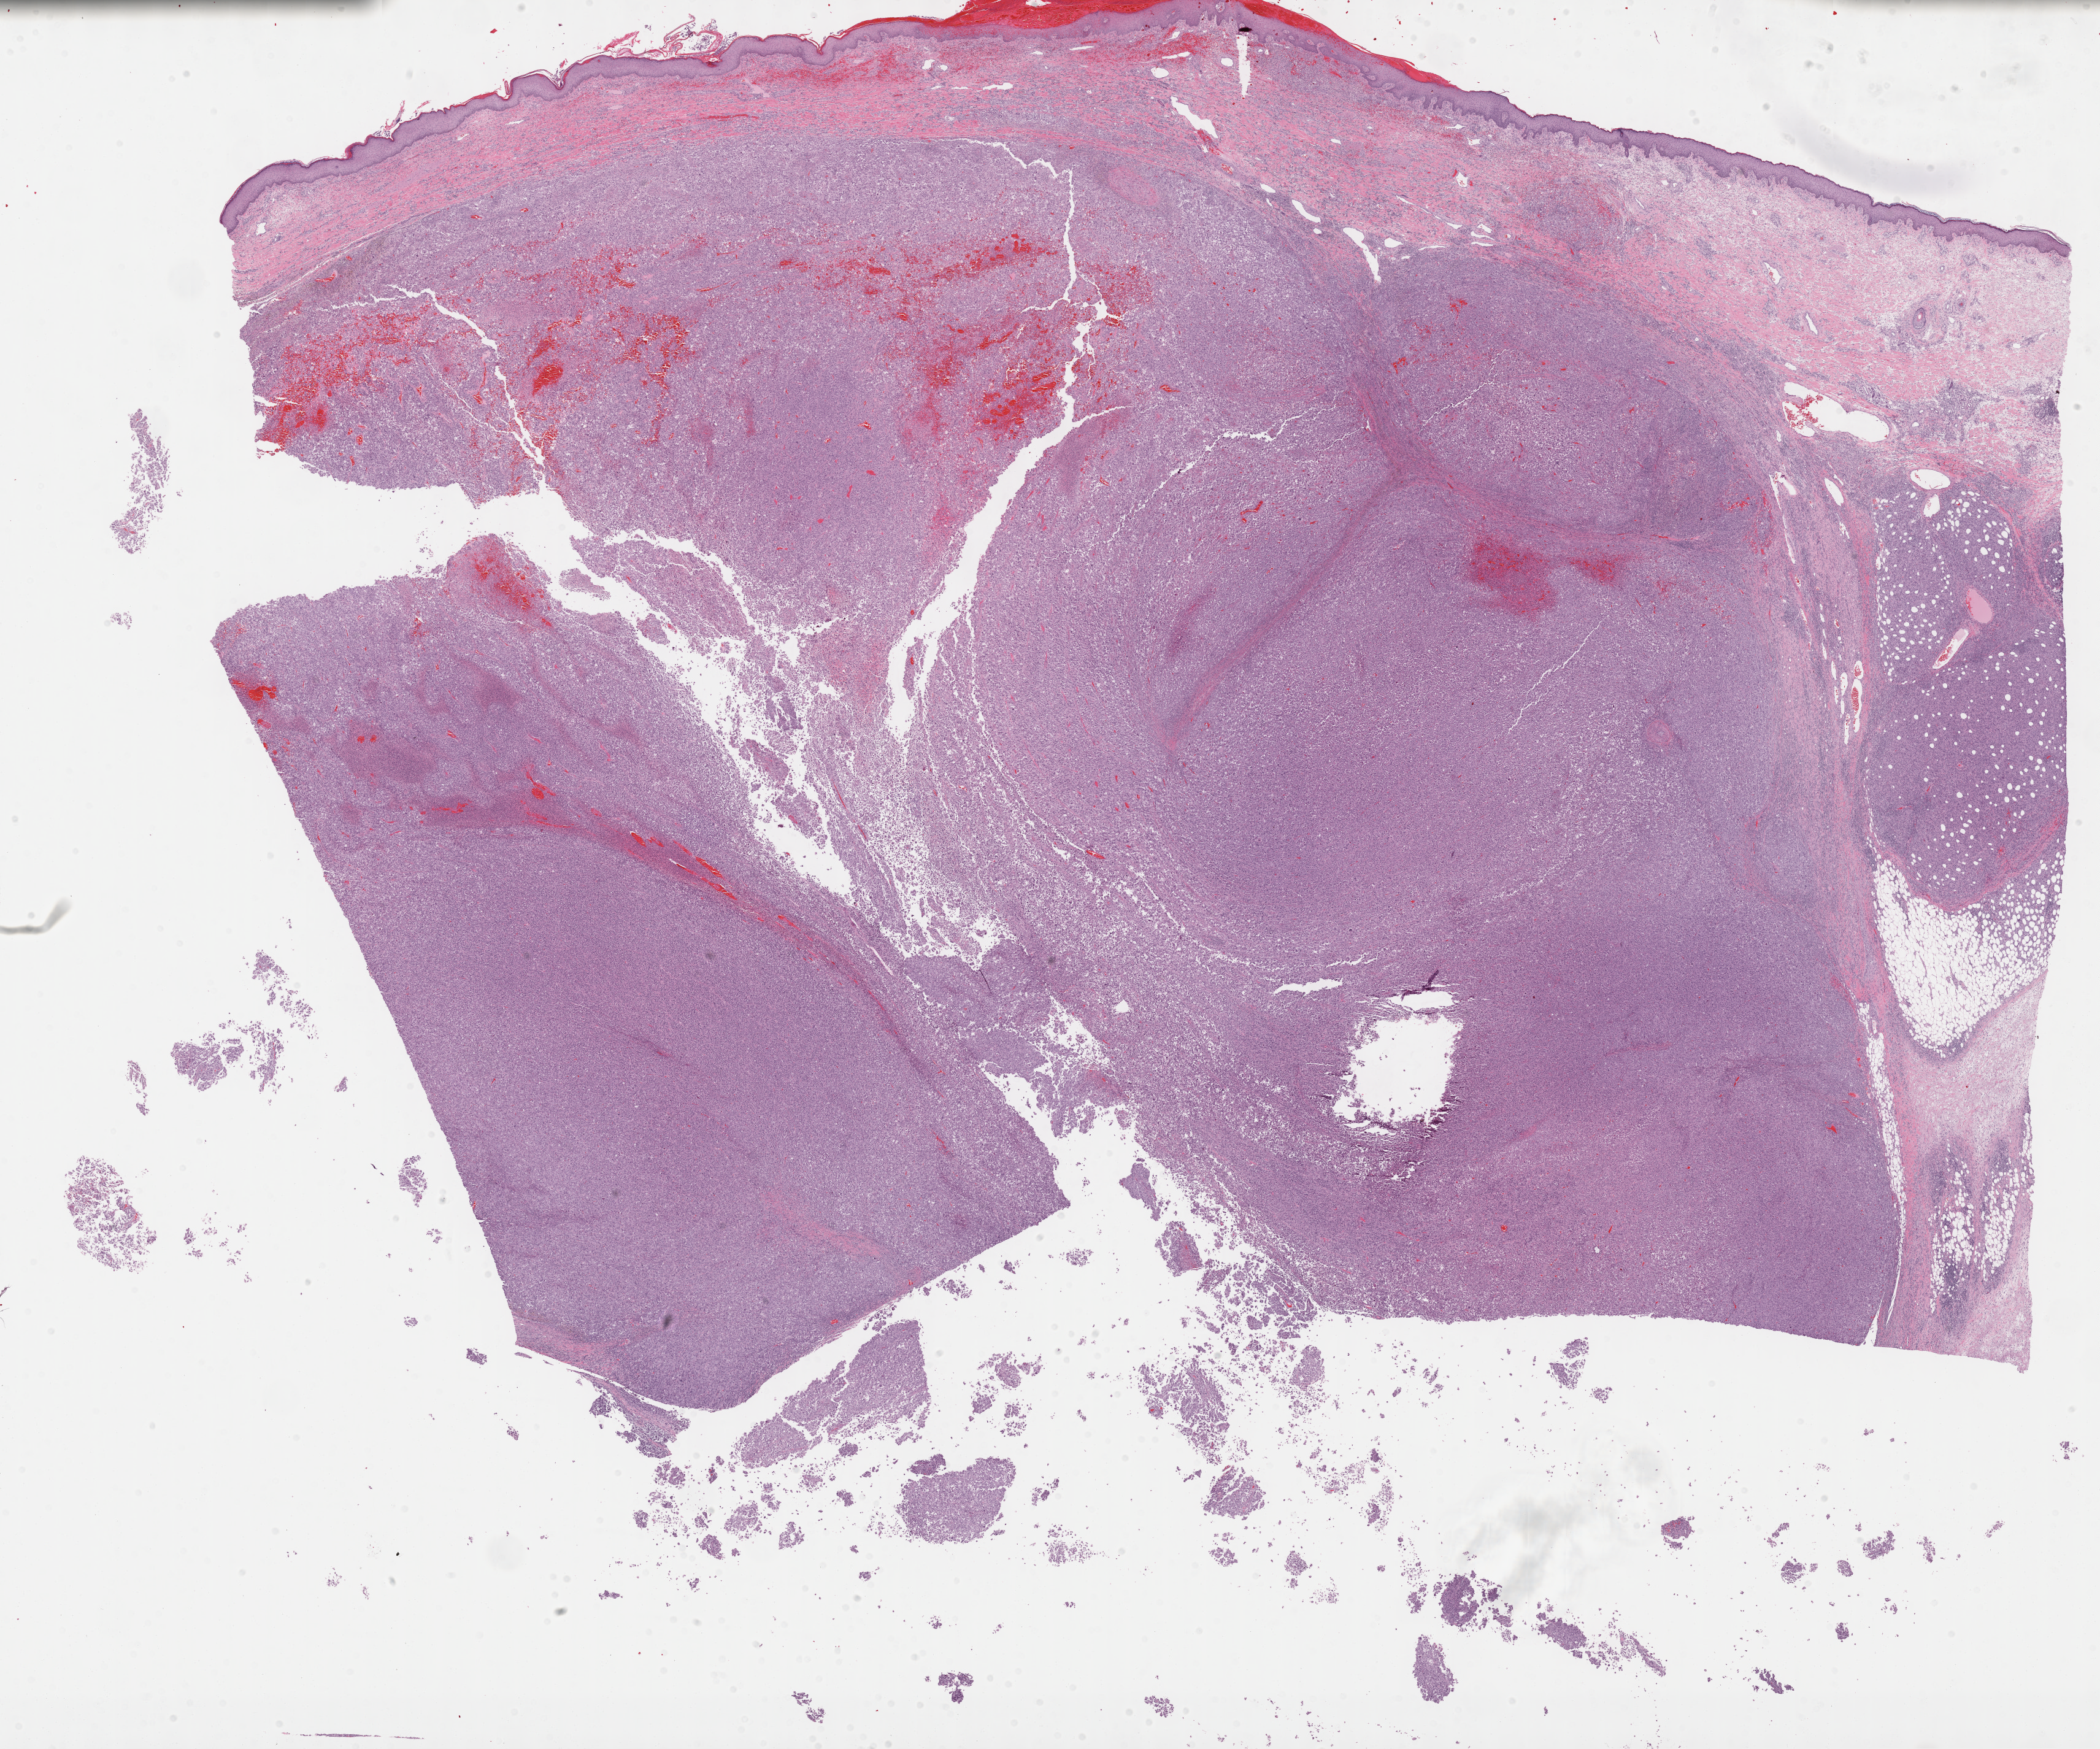
Hematoxylin and eosin (H&E) stained whole-slide image — whole scanned area (about 27.7 x 23.1 mm, slide scanned at 40x) shown as a low-resolution overview; formalin-fixed paraffin-embedded (FFPE) diagnostic section; connective, subcutaneous and other soft tissues, primary tumour sample. Patient: female, age at initial diagnosis 73 years.
Histologic diagnosis: Undifferentiated sarcoma (connective, subcutaneous and other soft tissues of lower limb and hip).